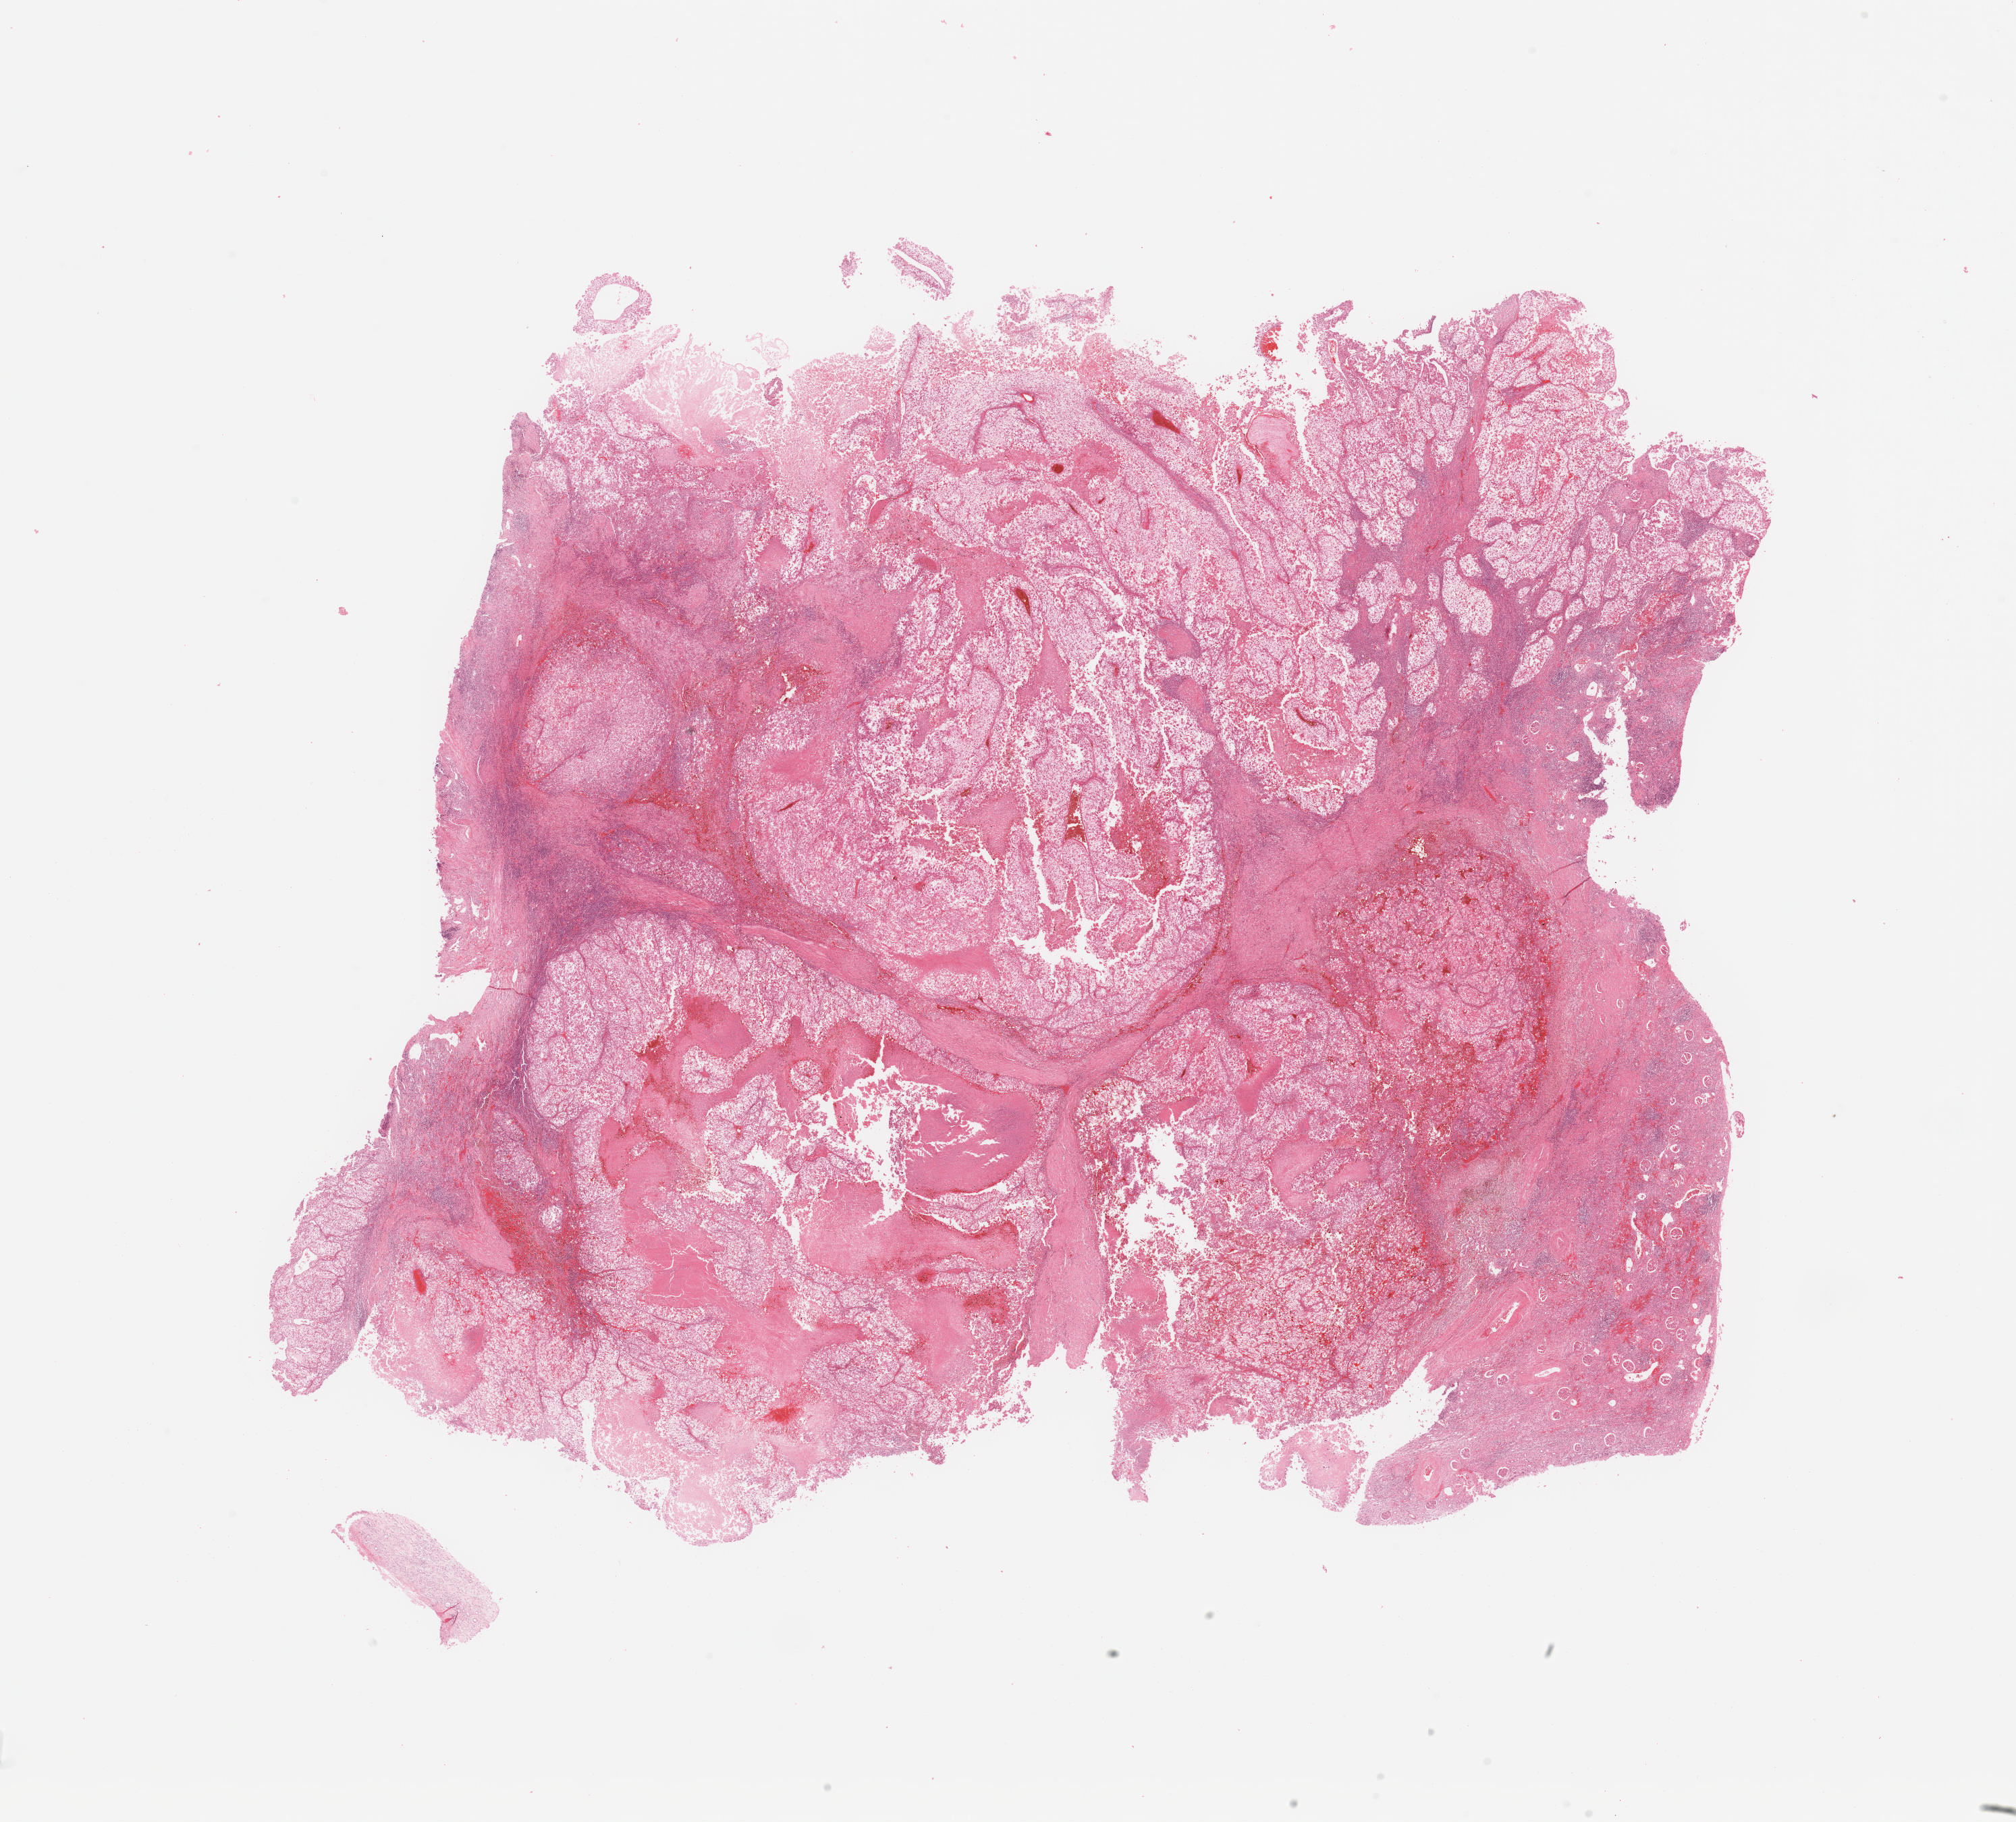
Whole-slide histology image, H&E-stained, shown as a low-resolution overview of the whole scanned area (about 23.6 x 21.3 mm, acquisition: 20x scan), tumour tissue sample, sampled site: kidney. 52-year-old female patient.
Diagnosis: Renal cell carcinoma, NOS.